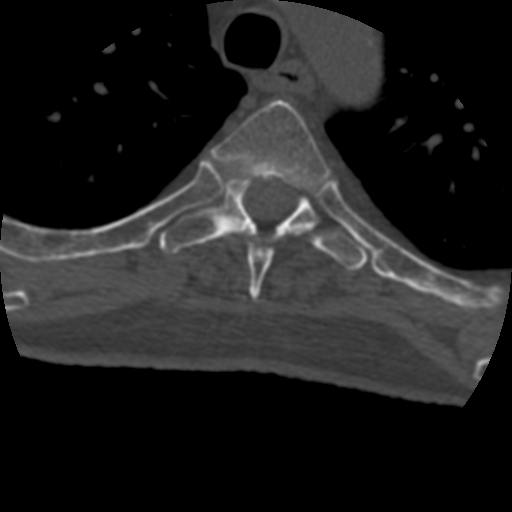
CT including the spine, one axial slice. Reconstruction kernel STANDARD. 120 kVp. Bone window (W 1800 / L 400 HU). 1.25 mm slice thickness. 512 × 512 image matrix. Patient age 69 years. Case-level facts recorded for this patient, not image findings: primary cancer: prostate.
Outlined on this slice (semi-automatic segmentation, software-assisted and operator-edited):
- T4 vertebra: bounding box (x1, y1, x2, y2) in pixels: (211, 100, 329, 302)
- T5 vertebra: (159, 175, 371, 271)